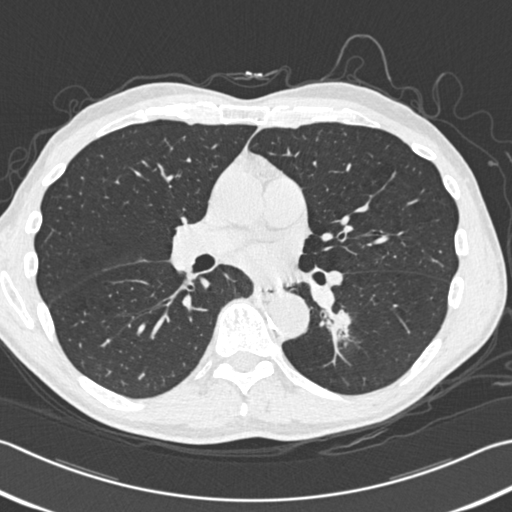
Low-dose screening chest CT, one axial slice. Position 188 of 354 along the scan axis. Reconstruction kernel B30f. 120 kVp. Lung window (W 1500 / L -600 HU). 512 × 512 image matrix, field of view 346 × 346 mm.
Outlined on this slice (expert manual segmentation):
- lesion 1 (tumor, lower lobe of left lung): bounding box [x1, y1, x2, y2] px = [334, 310, 351, 331]